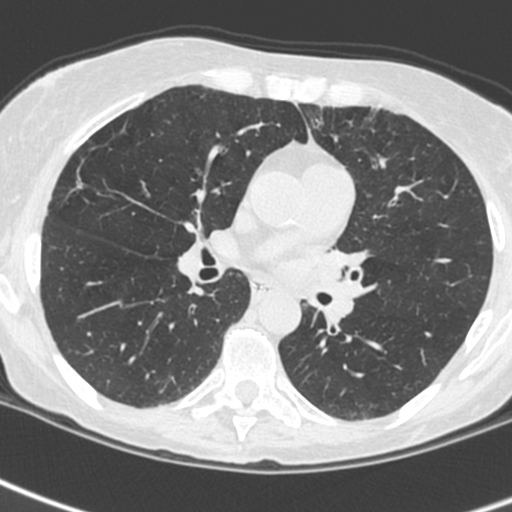
Low-dose screening chest CT, one axial slice; 120 kVp; lung window (W 1500 / L -600 HU); 1.3 mm slice thickness; 512 × 512 image matrix.
Structures marked on this image (outlined manually by an expert reader):
- lesion 3 (tumor, upper lobe of left lung): bounding box (x1, y1, x2, y2) in pixels: (306, 250, 364, 330)